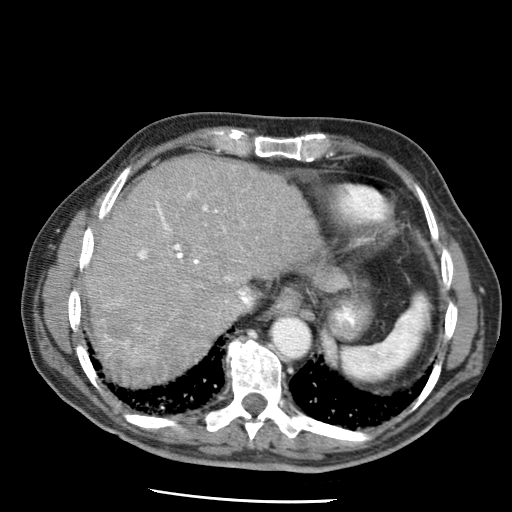
Contrast-enhanced abdominal CT (liver protocol), one axial slice. Position 54 of 79 along the scan axis. Reconstruction kernel STANDARD. Soft-tissue window (W 400 / L 40 HU). 2.5 mm slice thickness. 512 × 512 image matrix, field of view 320 × 320 mm. Case-level facts recorded for this patient, not image findings: diagnosis: hepatocellular carcinoma (patient treated with transarterial chemoembolisation; whether this scan precedes or follows treatment is not stated here); TNM stage (as recorded): Stage-IIIA; Child-Pugh class: A; tumour differentiation: moderately differentiated; tumour nodularity: multinodular.
Annotated regions visible in this slice (semi-automatically segmented with operator editing):
- abdominal aorta: bounding box <273,318,309,357> (left, top, right, bottom; pixels)
- liver parenchyma outside the tumour (the mass and vessels are separate outlines, so this box may not span the whole liver): <84,156,322,382>
- liver vessels: <105,193,241,353>